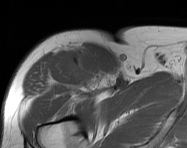
MRI of an extremity soft-tissue mass, one axial slice; position 109 of 114 along the scan axis; MR volume resampled by the dataset authors to the PET/CT grid (not the native acquisition matrix); 3.27 mm slice thickness; 187 × 148 image matrix, field of view 183 × 145 mm. Male patient. Case-level facts recorded for this patient, not image findings: histological type: pleiomorphic leiomyosarcoma; grade: intermediate; site of the primary tumour: right thigh.
Structures marked on this image (expert contour drawn on MRI and transferred to this co-registered scan by the dataset authors):
- gross tumour volume including surrounding oedema: bounding box <70,50,106,89> (left, top, right, bottom; pixels)
- gross tumour volume (mass): <86,61,105,85>